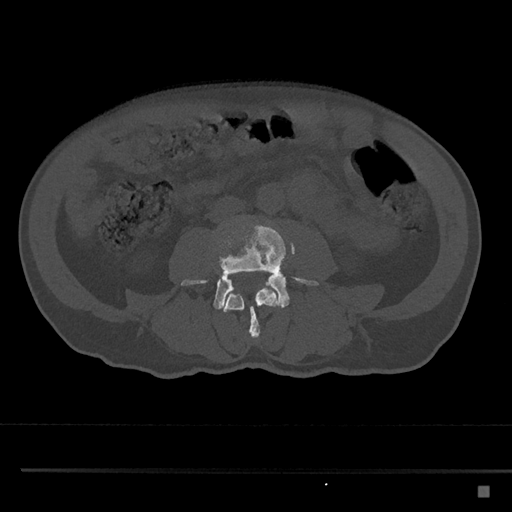
CT including the spine, one axial slice; slice 662 of 797 in the series (ordered by position); reconstruction kernel Br40s/3; 120 kVp; bone window (W 1800 / L 400 HU); 0.5 mm slice thickness; 512 × 512 image matrix, field of view 391 × 391 mm. Male patient, age 59 years. From the clinical record (not read from this slice): primary cancer: prostate.
Annotated regions visible in this slice (semi-automatic segmentation, software-assisted and operator-edited):
- L3 vertebra: bounding box (x1, y1, x2, y2) in pixels: (222, 284, 281, 338)
- L4 vertebra: (181, 222, 319, 310)